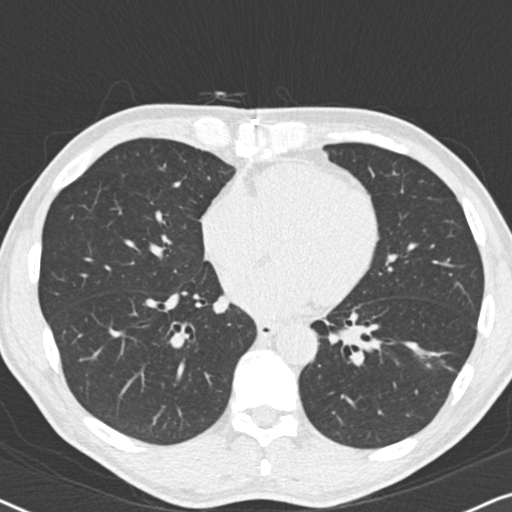
Low-dose screening chest CT, axial slice; second annual screen; lung window (W 1500 / L -600 HU); 2 mm slice thickness; standard (soft-tissue) reconstruction kernel (B30f); 512 × 512 image matrix, field of view 330 × 330 mm. Male, age 59 years at enrolment. Current smoker at enrolment.
Lesion marked by an expert reader, bounding box <409,333,467,384> (left, top, right, bottom; pixels). The screening reader recorded 2 non-calcified nodules or masses ≥4 mm on this exam (left lower lobe, right middle lobe); which of them this box marks is not recorded. Later outcome: lung cancer diagnosed 484 days after this screen (after the third annual screen) — adenocarcinoma, NOS, left lower lobe, poorly differentiated (G3), stage IA (AJCC 6th edition), 20 mm at pathology.